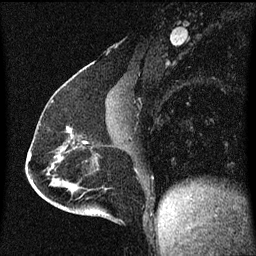
Breast MRI (dynamic contrast-enhanced), one sagittal slice; position 28 of 60 along the scan axis; dynamic contrast-enhanced series, image 2 of 3 at this slice position (ordered by acquisition); 1.5 T; TE 4.2 ms, TR 8 ms; 2 mm slice thickness; 256 × 256 image matrix. Female patient, age 51 years.
Annotated regions visible in this slice (semi-automatic segmentation, software-assisted and operator-edited):
- analysis volume of interest (the breast-tissue region the enhancement analysis was run in; not a lesion): bounding box [x1, y1, x2, y2] px = [62, 126, 93, 149]
- tumour enhancement mask (voxels above the 70 % enhancement threshold inside the analysis volume of interest): [66, 126, 89, 145]